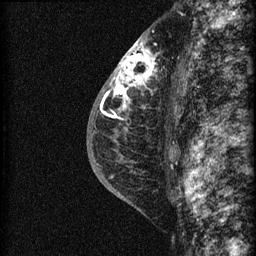
Breast MRI (dynamic contrast-enhanced), one sagittal slice. Position 41 of 60 along the scan axis. Dynamic contrast-enhanced series, image 2 of 3 at this slice position (ordered by acquisition). 1.5 T. TE 4.2 ms, TR 22.7 ms. 1.5 mm slice thickness. 256 × 256 image matrix, field of view 180 × 180 mm. Female patient, age 48 years. From the clinical record (not read from this slice): setting: breast cancer imaged before/during neoadjuvant chemotherapy; receptor status: triple-negative.
Structures marked on this image (semi-automatically segmented with operator editing):
- analysis volume of interest (the breast-tissue region the enhancement analysis was run in; not a lesion): bounding box (x1, y1, x2, y2) in pixels: (115, 34, 169, 162)
- tumour enhancement mask (voxels above the 90 % enhancement threshold inside the analysis volume of interest): (115, 40, 156, 117)